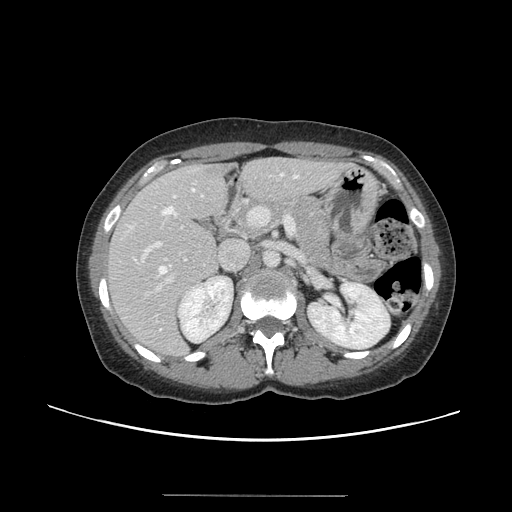
Contrast-enhanced abdominal CT, one axial slice; slice 77 of 144 in the series (ordered by position); 120 kVp; intravenous contrast given; soft-tissue window (W 400 / L 40 HU); 2.5 mm slice thickness; 512 × 512 image matrix, field of view 380 × 380 mm. Female patient, age 53 years. Case-level facts recorded for this patient, not image findings: diagnosis: colorectal cancer liver metastases, imaged before liver resection; multiple liver metastases: yes; largest metastasis: 1.1 cm; disease in both lobes: no.
Structures marked on this image (manually delineated by an expert):
- hepatic veins: box from (x=159, y=173) to (x=298, y=330) px
- liver: (x=108, y=159)–(x=344, y=356)
- planned liver remnant (the part of the liver to remain after resection): (x=109, y=159)–(x=318, y=299)
- portal vein (with intrahepatic branches): (x=133, y=200)–(x=295, y=291)